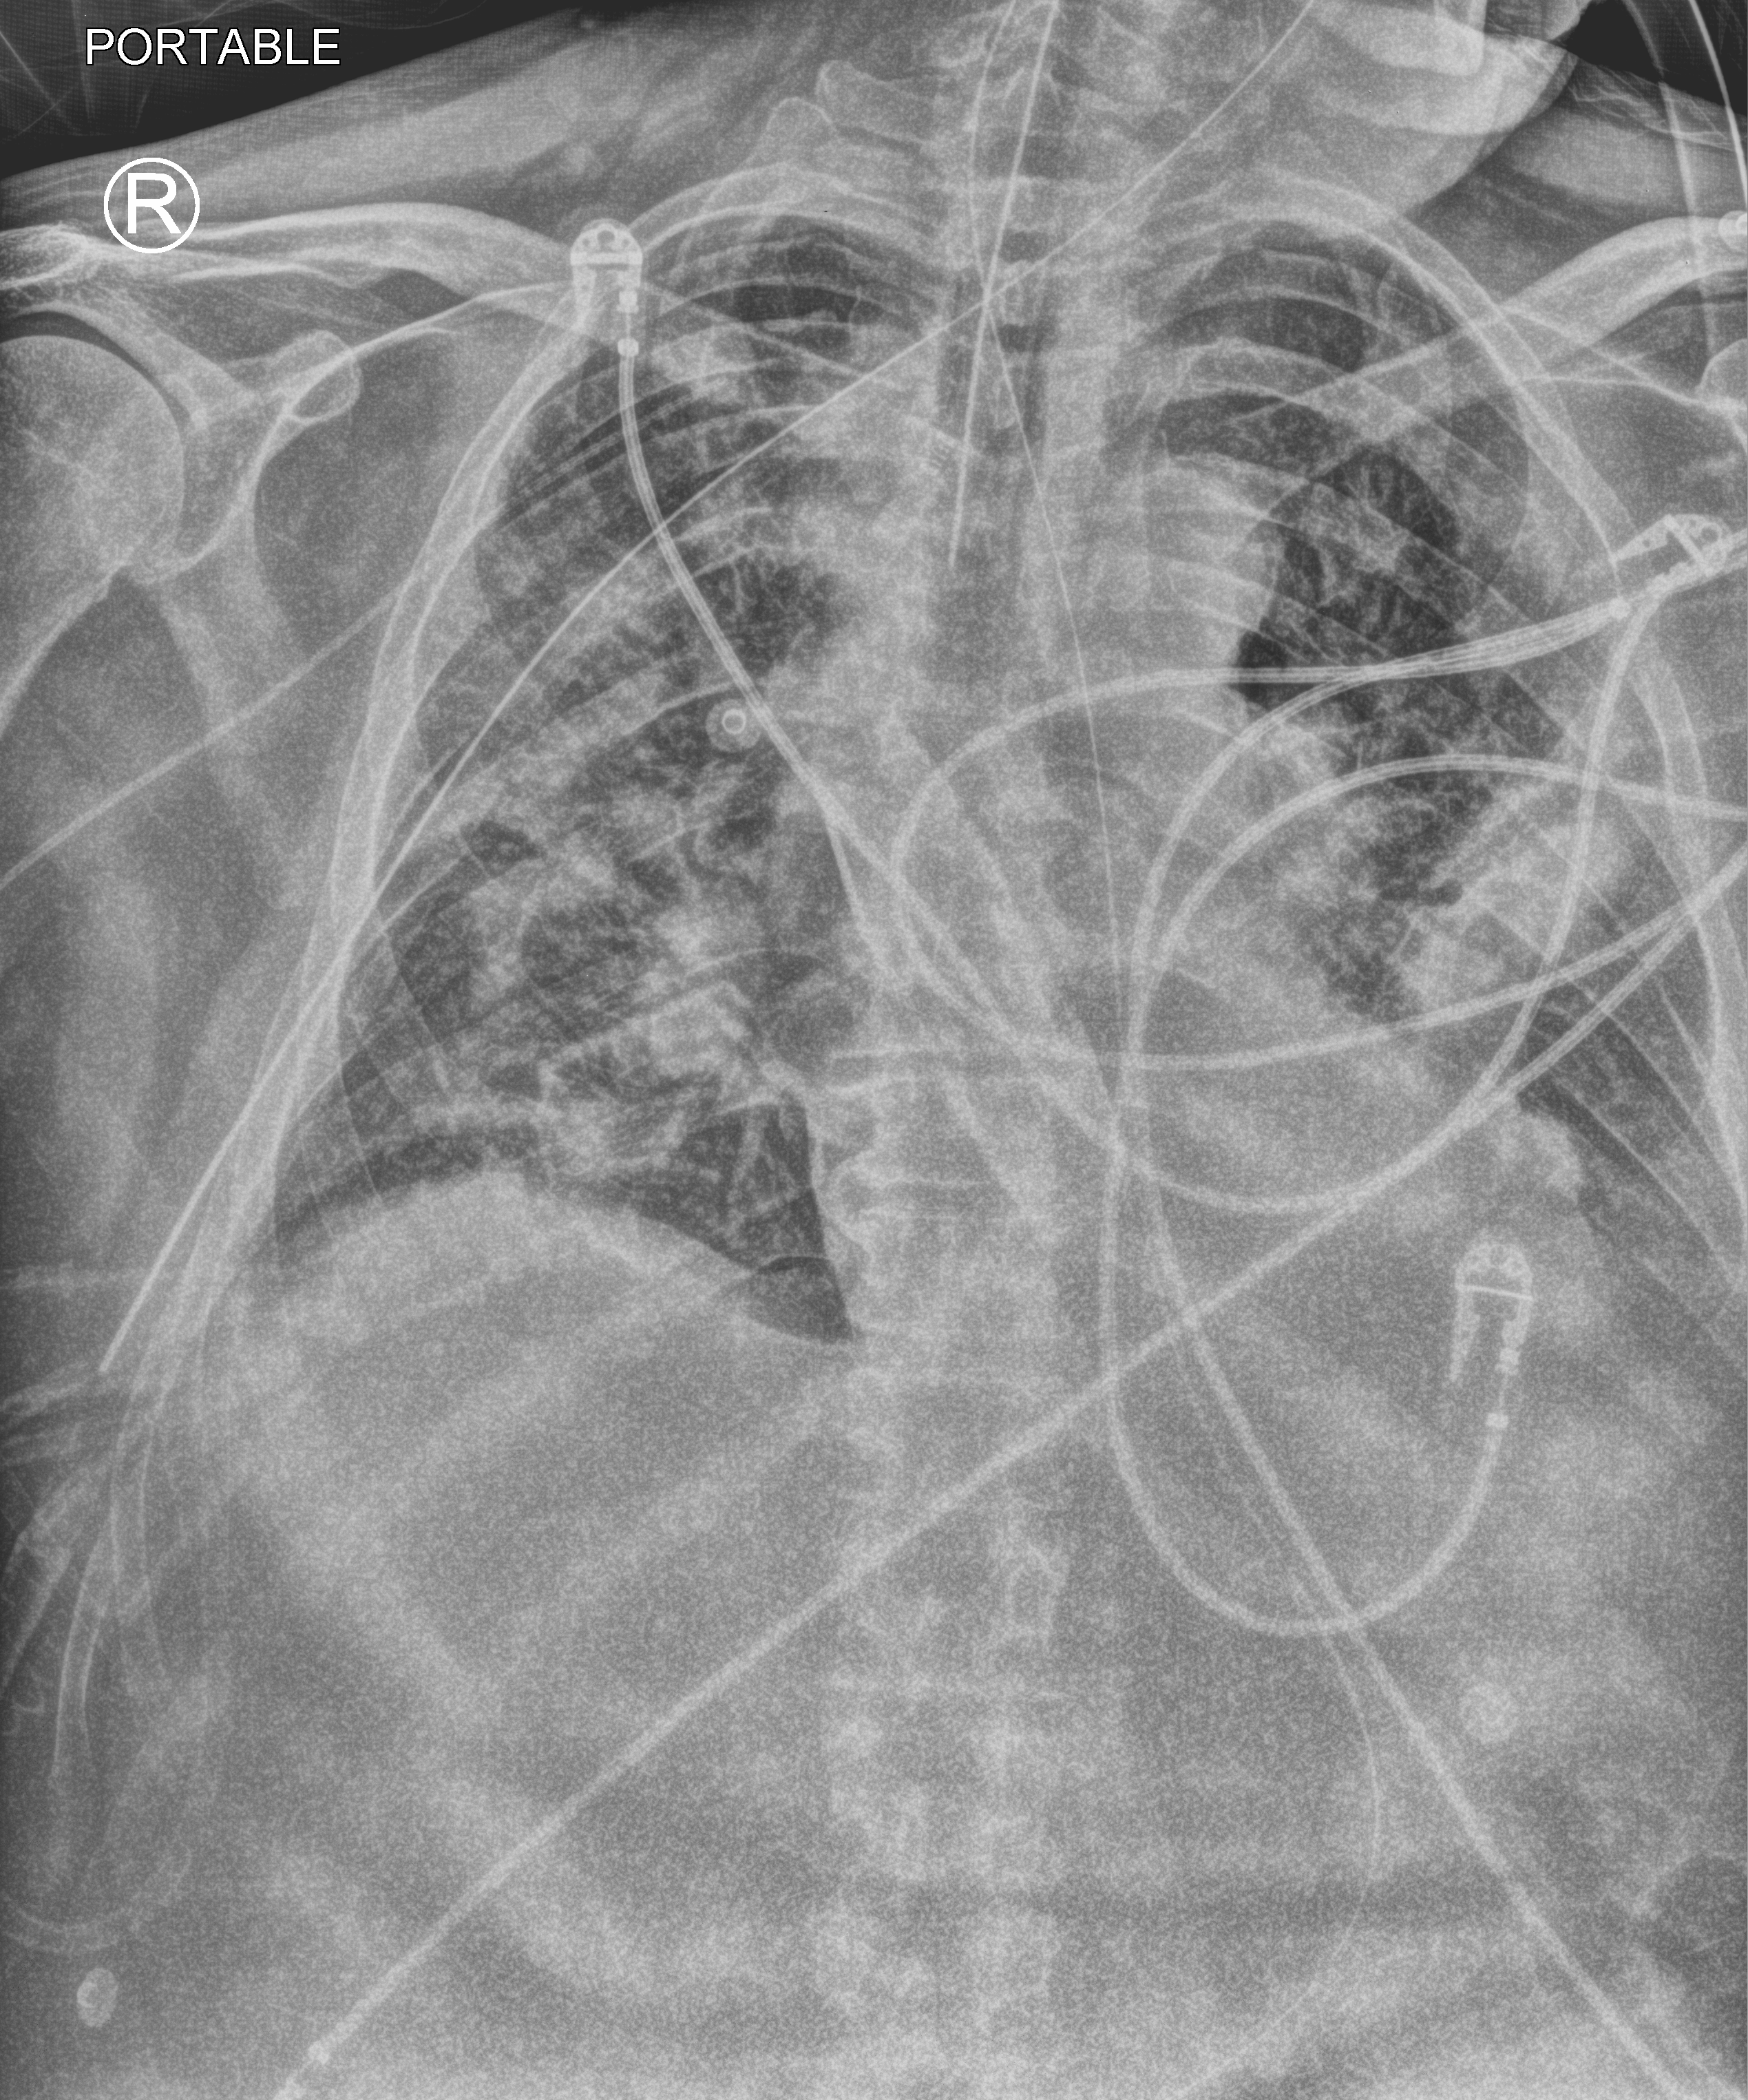
Bedside chest radiograph (computed radiography); anteroposterior (AP) projection. Patient hospitalised with COVID-19; male, aged 60–74 years.
From the hospital-stay record, not from the radiograph (when in the stay this image was taken is not recorded):
- mechanically ventilated during this hospital stay: yes